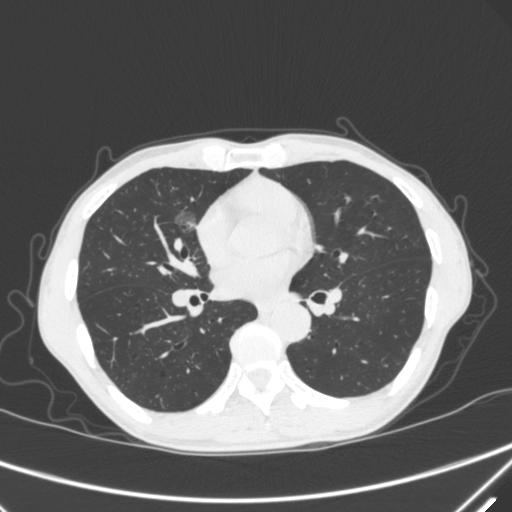
Chest CT, one axial slice; position 165 of 340 along the scan axis; lung window (W 1500 / L -600 HU); 1 mm slice thickness; 512 × 512 image matrix. Patient: male, 67 years. From the clinical record (not read from this slice): clinical TNM (as recorded): T1c N0 M0; histopathological grade: G1-2.
Outlined on this slice (bounding box drawn by a radiologist):
- lung tumour (recorded histology: adenocarcinoma): bounding box [x1, y1, x2, y2] px = [167, 198, 198, 242]